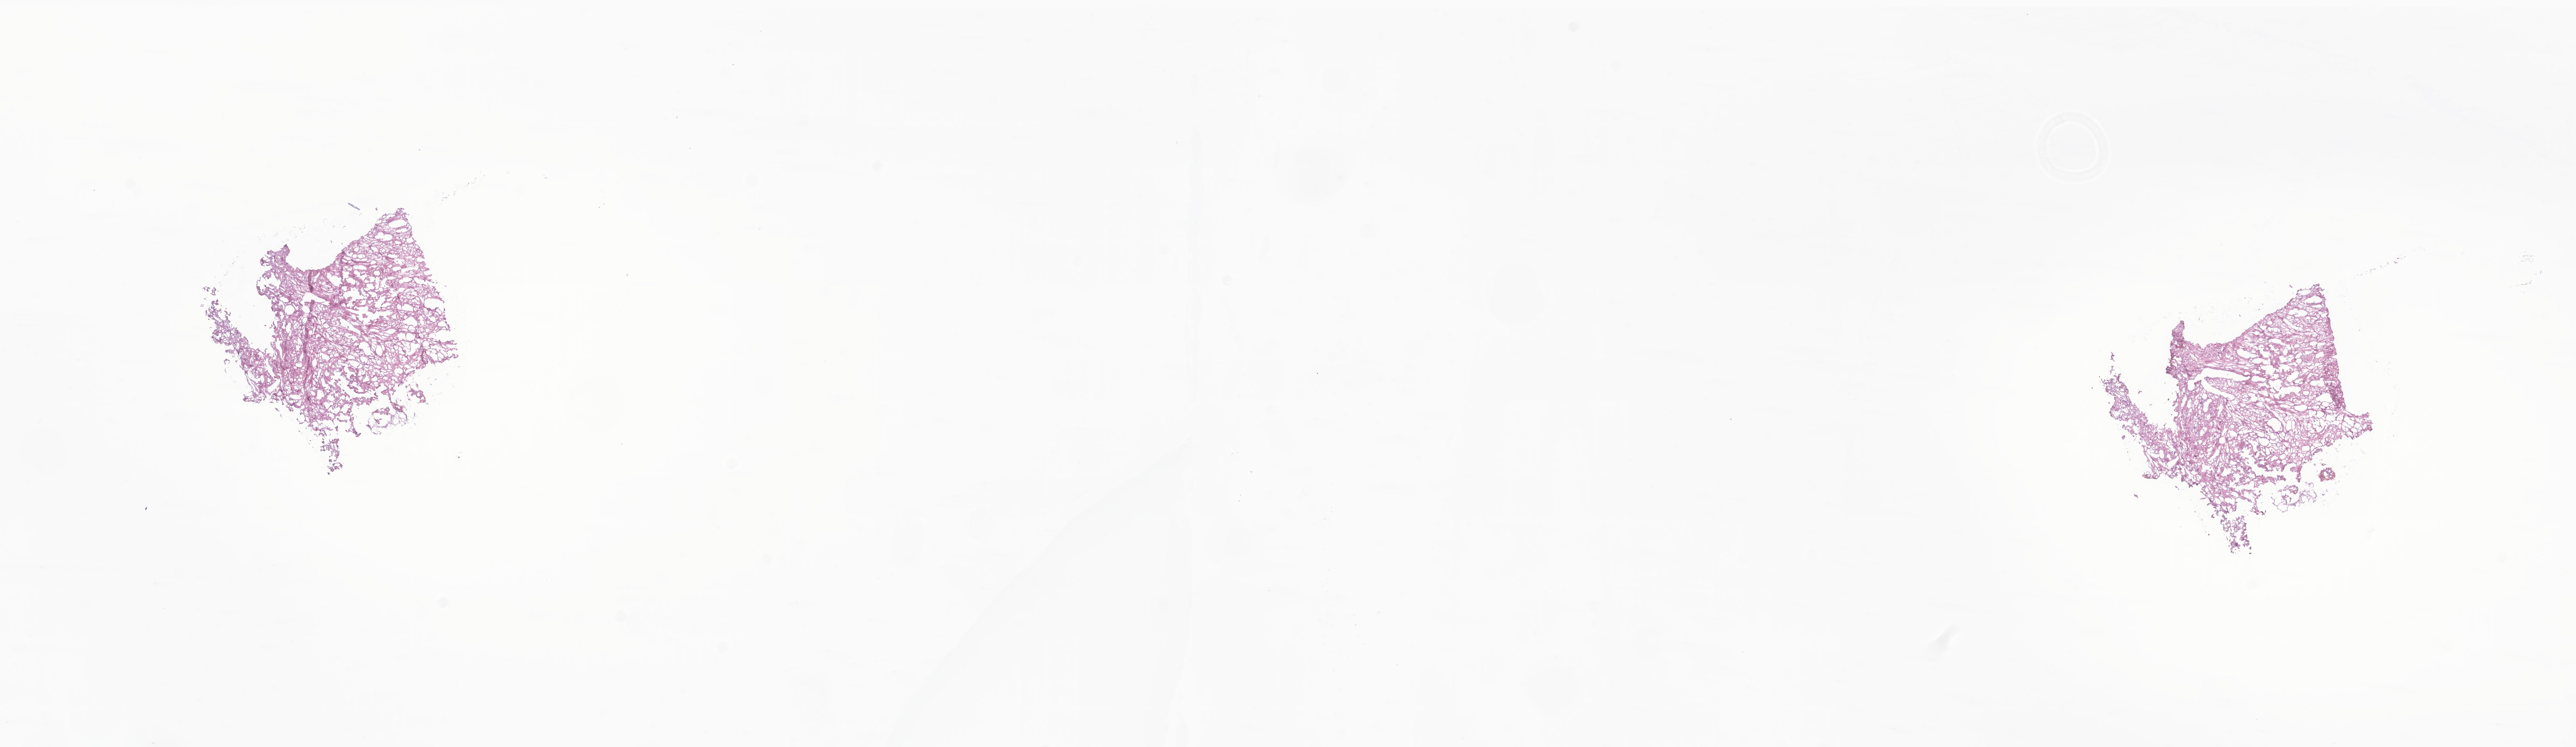
Digitized H&E-stained section of tumor tissue from the urinary bladder, whole scanned area (about 23.5 x 6.8 mm) shown as a low-resolution overview; frozen section (OCT-embedded). Patient: female, age 122 months.
Diagnosis (ICD-O-3 morphology term): Myofibroblastic tumor, NOS.